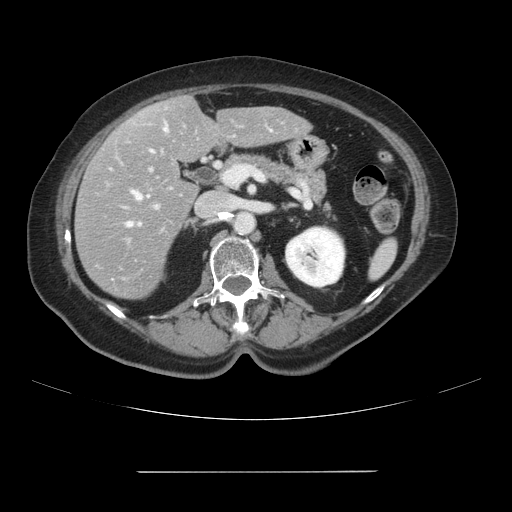
Contrast-enhanced abdominal CT, one axial slice; slice 46 of 111 in the series (ordered by position); intravenous contrast given; soft-tissue window (W 400 / L 40 HU); 2.5 mm slice thickness; 512 × 512 image matrix, field of view 400 × 400 mm. Female patient, age 74 years. Case-level facts recorded for this patient, not image findings: diagnosis: colorectal cancer liver metastases, imaged before liver resection; multiple liver metastases: yes; largest metastasis: 1.1 cm; disease in both lobes: yes.
Structures marked on this image (expert manual segmentation):
- hepatic veins: box from (x=127, y=125) to (x=167, y=227) px
- liver: (x=75, y=97)–(x=310, y=299)
- planned liver remnant (the part of the liver to remain after resection): (x=142, y=97)–(x=310, y=163)
- portal vein (with intrahepatic branches): (x=154, y=206)–(x=158, y=208)